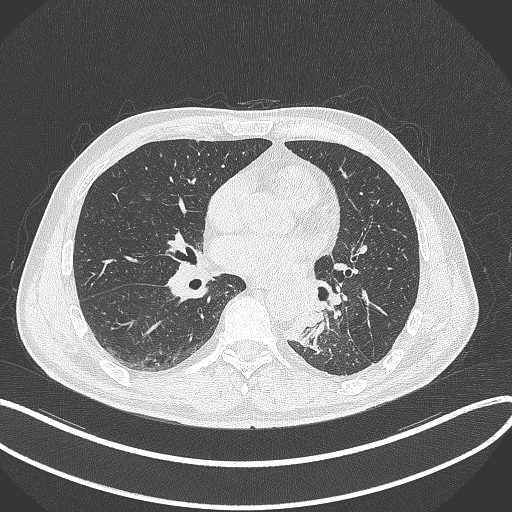
Chest CT, one axial slice; lung window (W 1500 / L -600 HU); 1 mm slice thickness; 512 × 512 image matrix, field of view 400 × 400 mm. Male patient, age 59 years. From the clinical record (not read from this slice): clinical TNM (as recorded): T2a N2 M0.
Annotated regions visible in this slice (rectangle marked by the reading radiologist):
- lung tumour (recorded histology: squamous cell carcinoma): box from (x=280, y=285) to (x=323, y=346) px